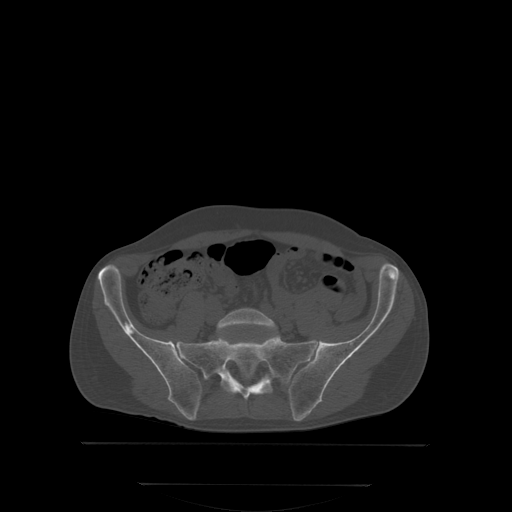
CT including the spine, one axial slice; position 85 of 350 along the scan axis; bone window (W 1800 / L 400 HU); 2.5 mm slice thickness; 512 × 512 image matrix, field of view 500 × 500 mm. Male patient, age 58 years. Case-level facts recorded for this patient, not image findings: primary cancer: prostate.
Structures marked on this image (semi-automatic segmentation, software-assisted and operator-edited):
- L5 vertebra: box from (x=217, y=308) to (x=276, y=329) px